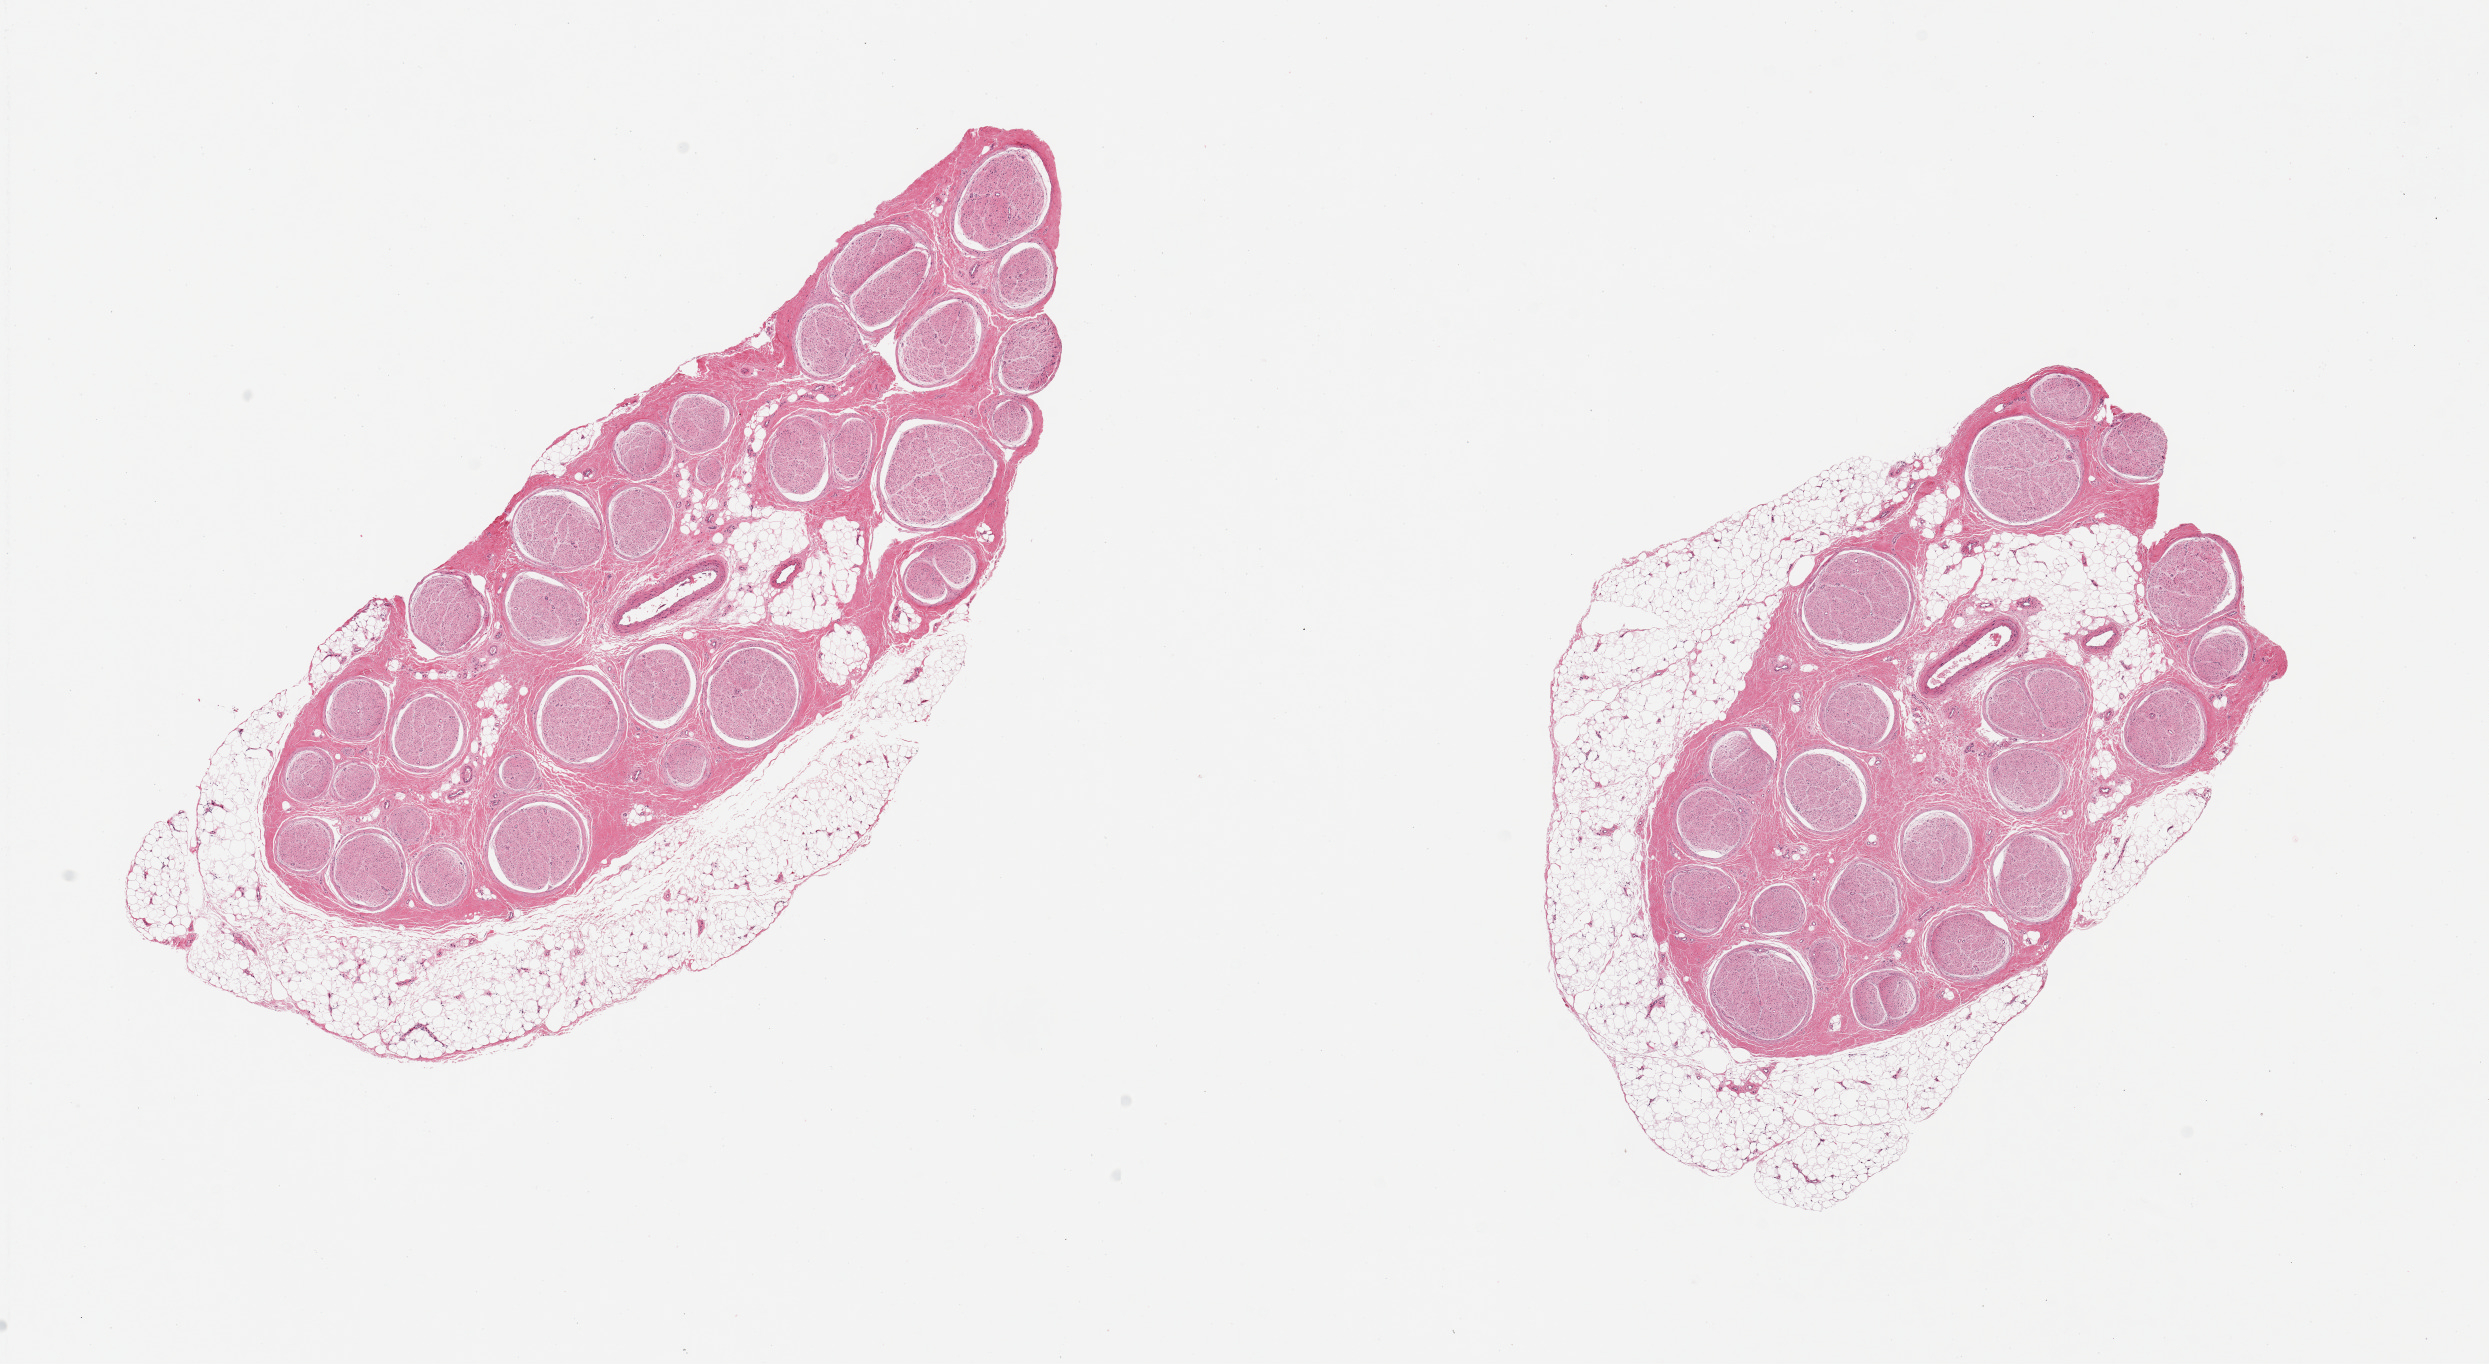
Hematoxylin and eosin (H&E) whole-slide image, low-resolution overview of the scanned area, about 19.7 x 10.8 mm; PAXgene-fixed paraffin-embedded (PFPE) section; target tissue: tibial nerve; donor tissue sample. Donor: male.
- reviewer comment on this tissue sample: 2 pieces, adherent partial rims of fat, up to ~1mm